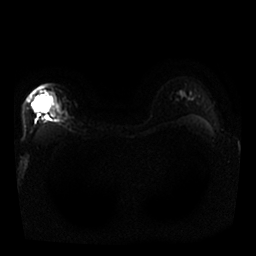
Breast MRI, one axial slice. Slice 19 of 25 in the series (ordered by position). Diffusion-weighted series; image 2 of 4 stored at this slice position (different b-values; order by instance number). 1.5 T. 256 × 256 image matrix, field of view 340 × 340 mm. Female patient.
Outlined on this slice (manually delineated by an expert):
- tumour on diffusion-weighted imaging: bounding box (x1, y1, x2, y2) in pixels: (32, 97, 41, 110)